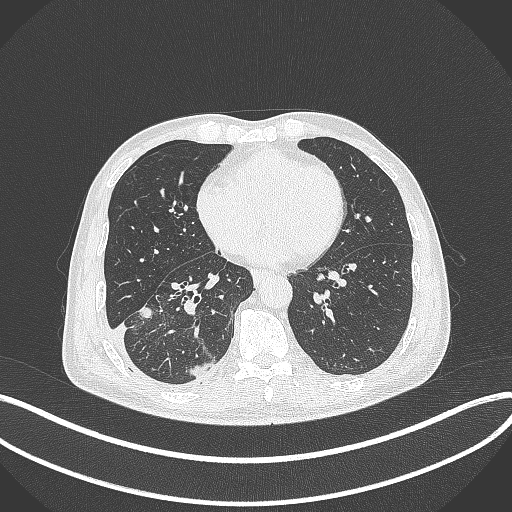
Chest CT, one axial slice. Position 149 of 388 along the scan axis. Reconstruction kernel B70f. Lung window (W 1500 / L -600 HU). 1 mm slice thickness. 512 × 512 image matrix, field of view 400 × 400 mm. Male patient, age 64 years. From the clinical record (not read from this slice): clinical TNM (as recorded): T3 N0 M0; histopathological grade: G2-3.
Structures marked on this image (rectangle marked by the reading radiologist):
- lung tumour (recorded histology: adenocarcinoma): box from (x=137, y=303) to (x=159, y=327) px